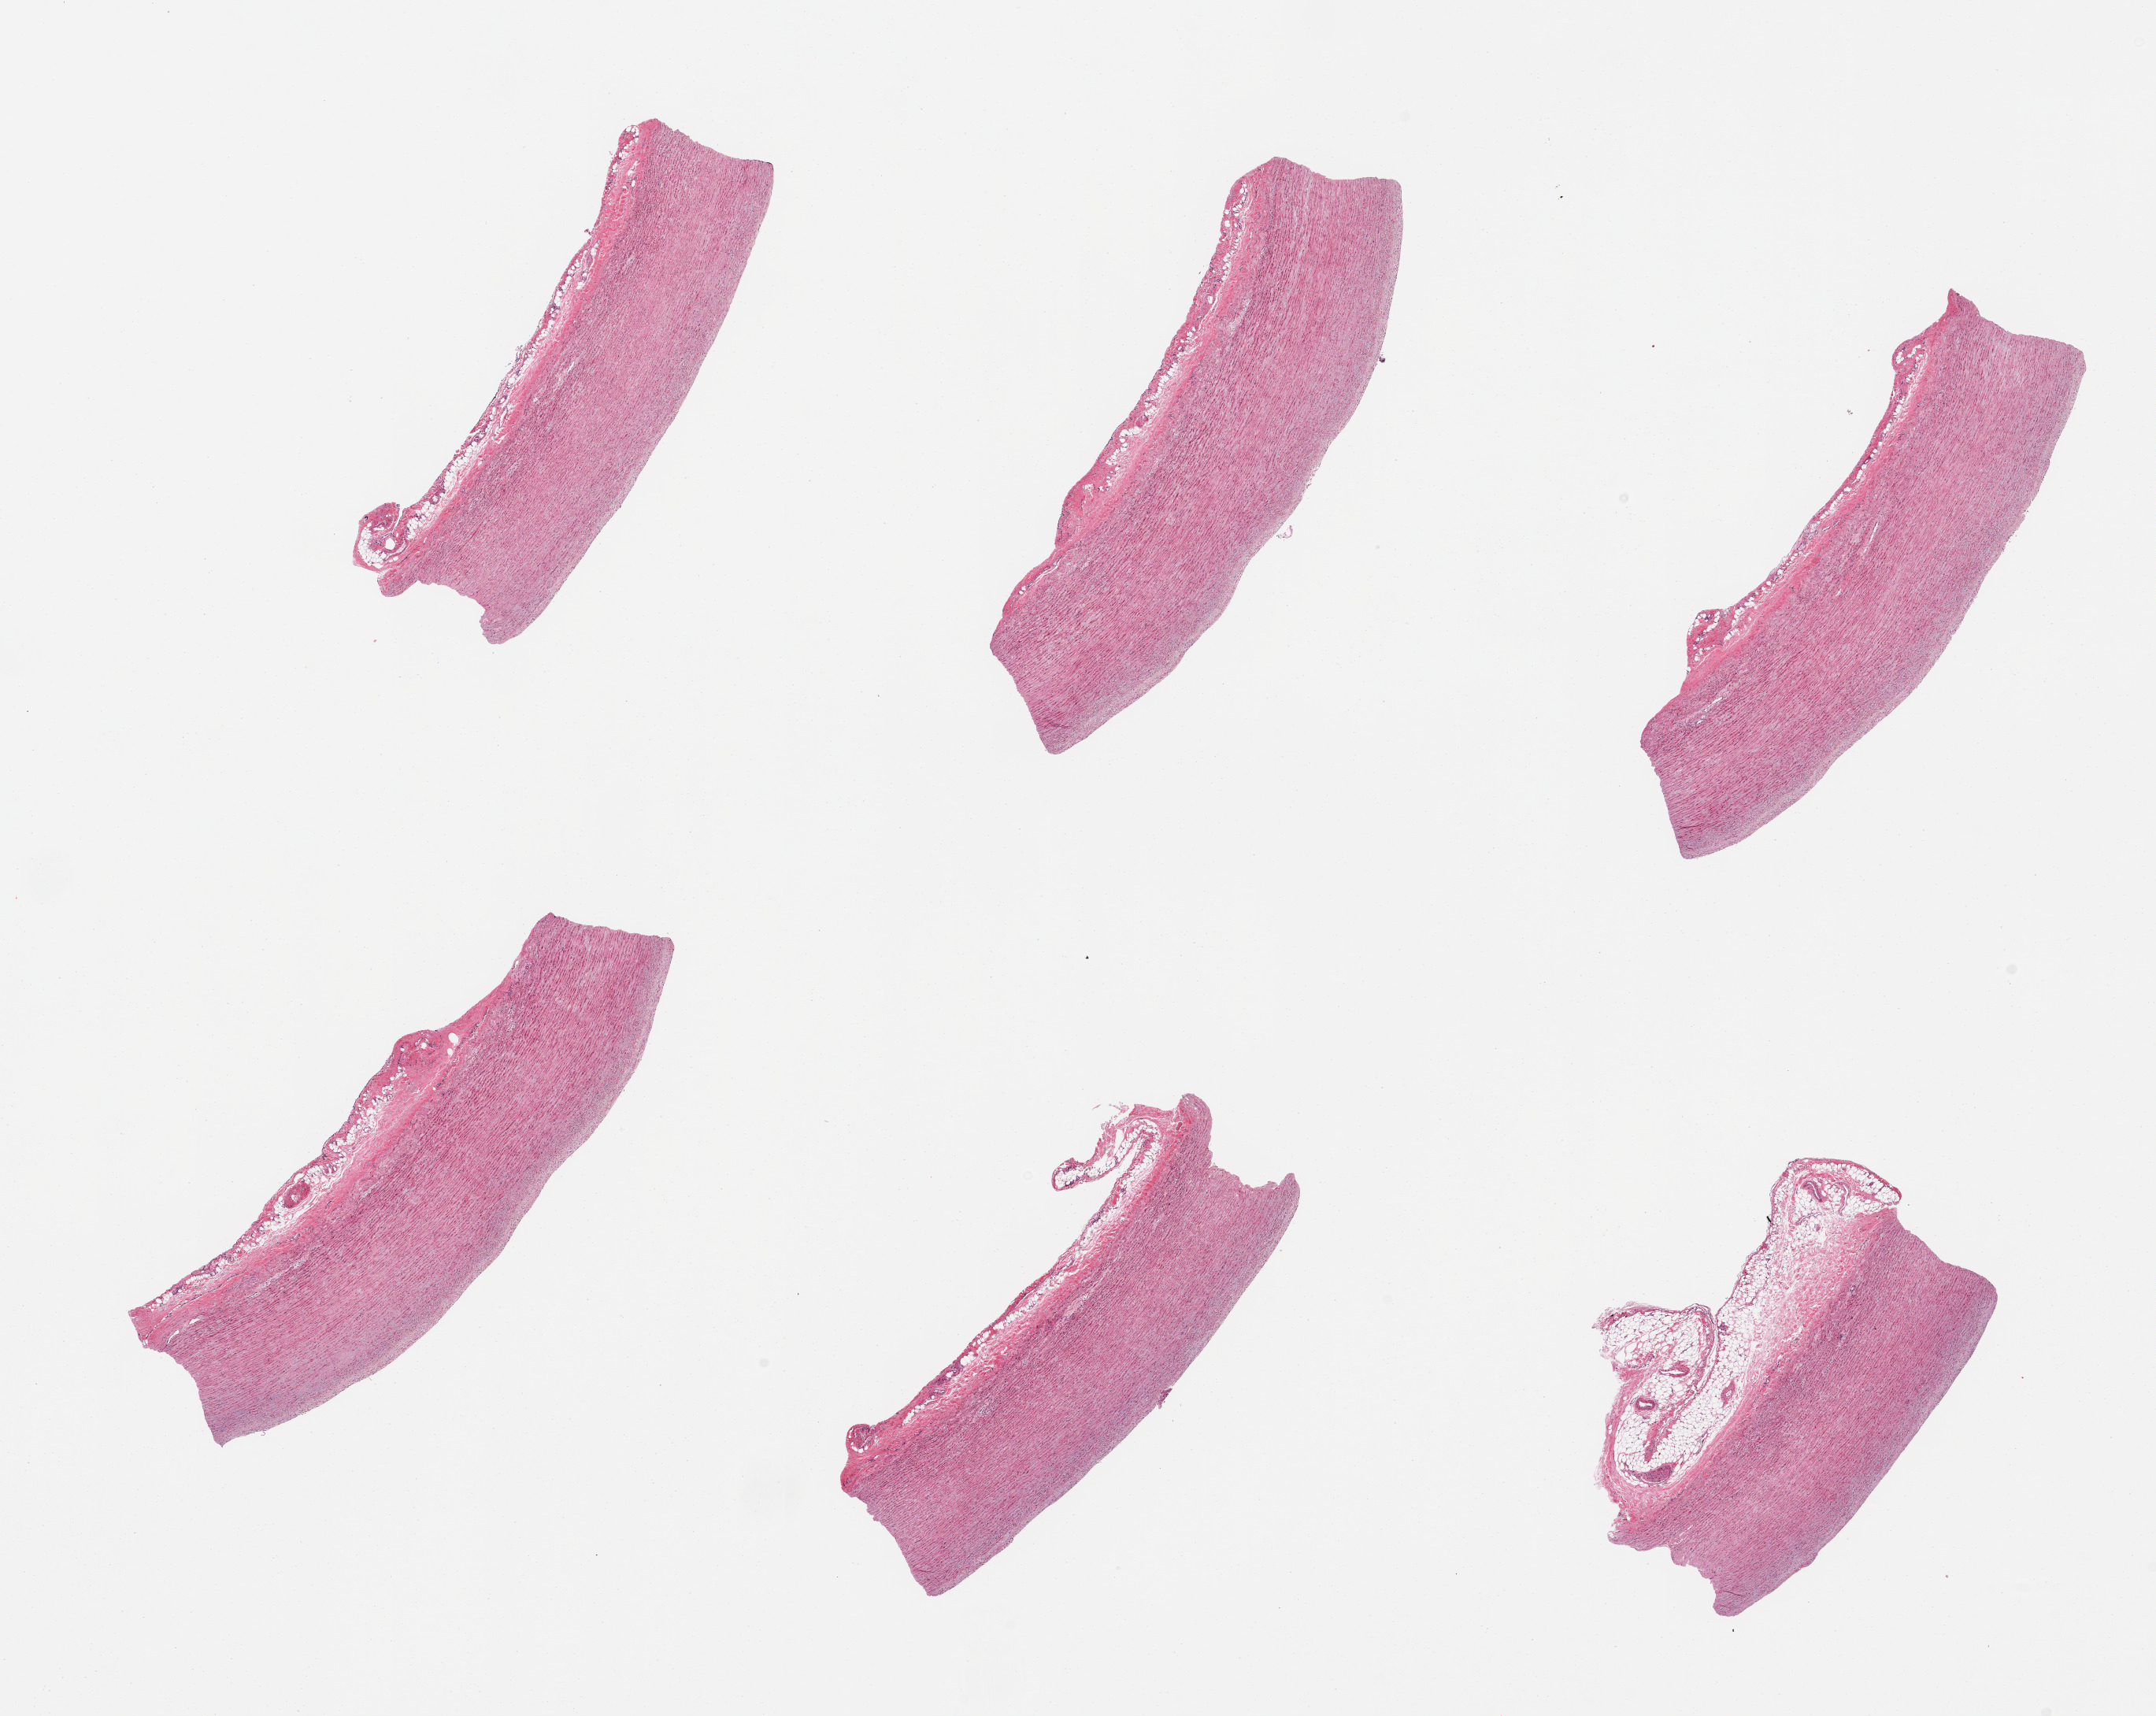
Whole-slide image, hematoxylin and eosin (H&E) stain, a low-resolution overview of the entire scanned area, about 21.7 x 17.2 mm (acquisition: 20x scan), PAXgene-fixed, paraffin-embedded tissue, section of aorta (target tissue), tissue donor sample. Donor sex: female.
Reviewer comment on this tissue sample: 6 pieces; no plaques; focal adventitial fat up to 0.5mm.